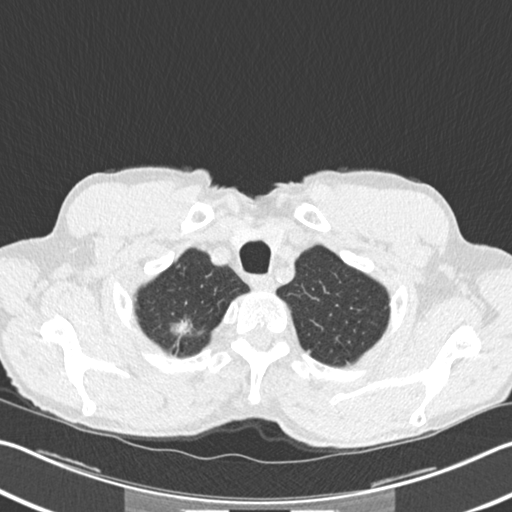
Axial slice from a low-dose chest CT screening exam. Second screening round (one year after baseline). Lung window (W 1500 / L -600 HU). 512 × 512 image matrix, field of view 342 × 342 mm. Male, age 62 years at enrolment. Former smoker at enrolment.
Expert reader's lesion annotation, bounding box <160,307,205,350> (left, top, right, bottom; pixels). The screening reader recorded 2 non-calcified nodules or masses ≥4 mm on this exam (right upper lobe, right upper lobe); which of them this box marks is not recorded.